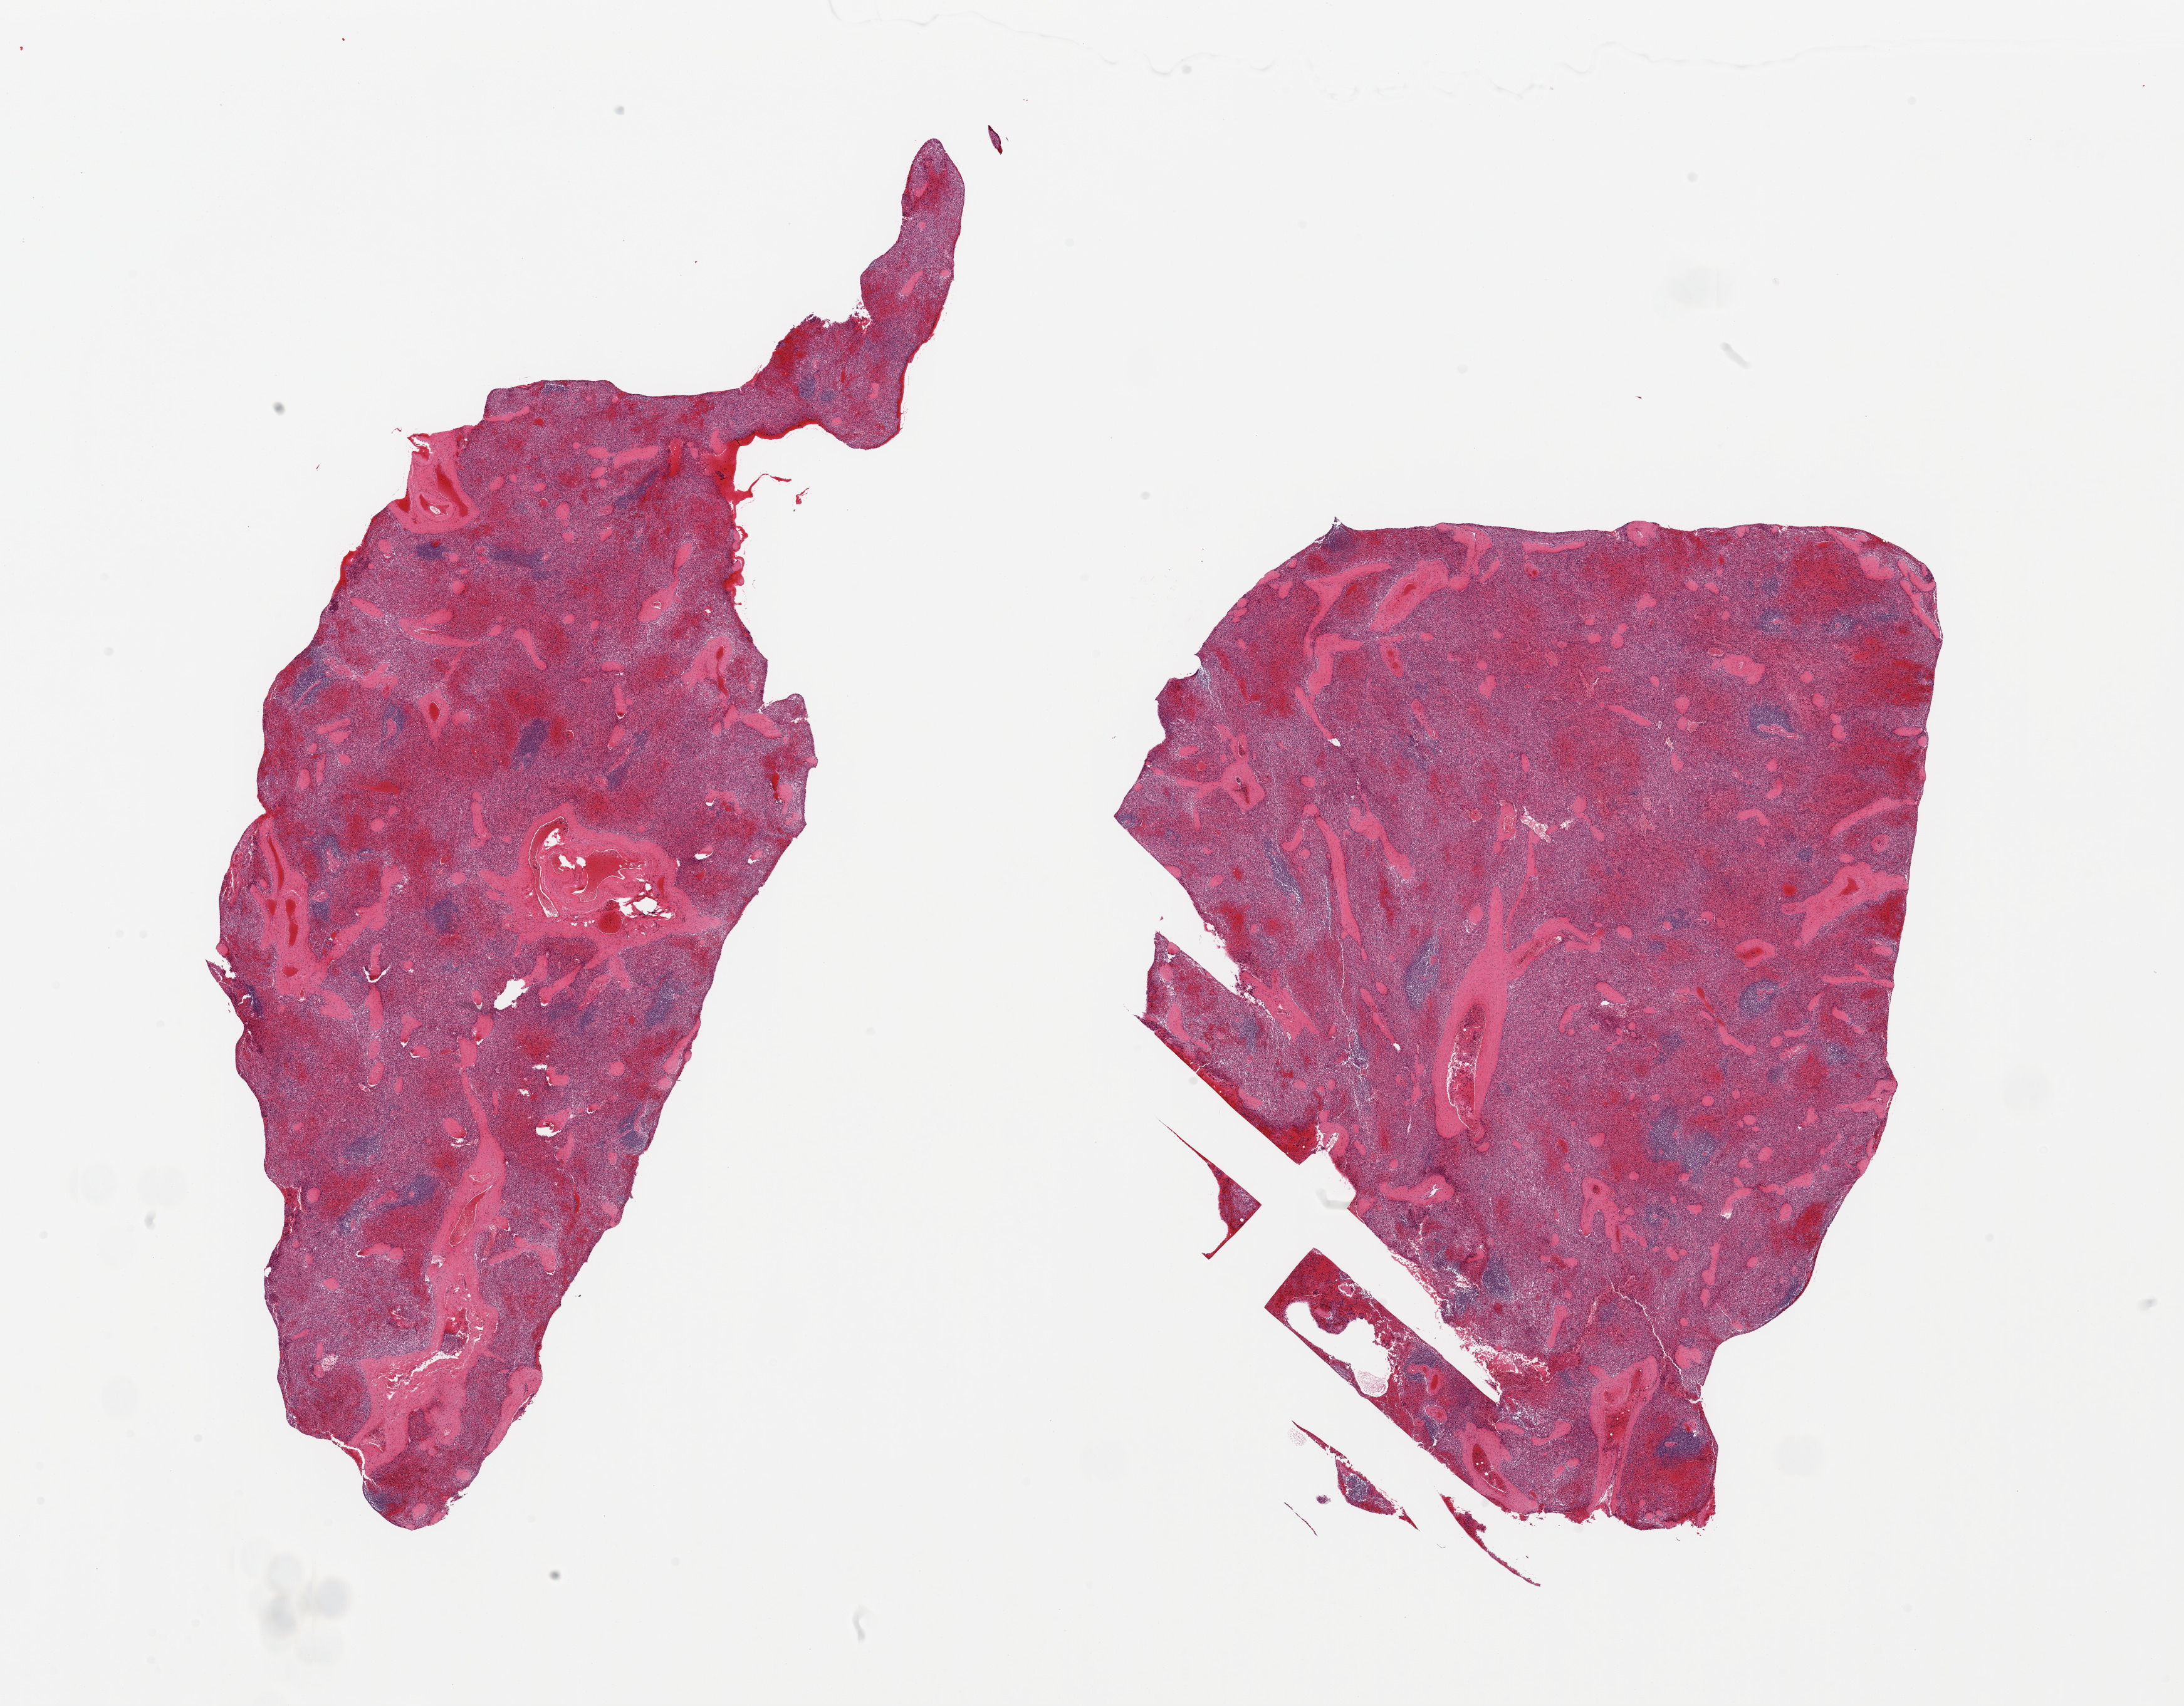
H&E whole-slide image — whole scanned area (about 27.6 x 21.5 mm, acquisition: 20x scan) shown as a low-resolution overview, PAXgene-fixed, paraffin-embedded tissue, sampled site (target tissue): spleen, tissue donor sample.
• pathologist's review note for this sample: 2 pieces, moderate congestion